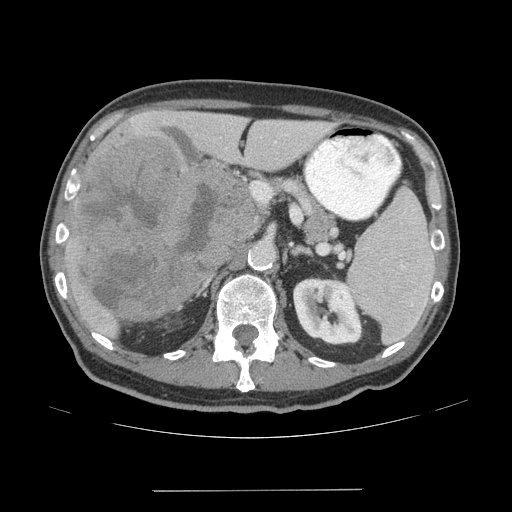
Contrast-enhanced abdominal CT (liver protocol), one axial slice; position 29 of 77 along the scan axis; reconstruction kernel STANDARD; 140 kVp; soft-tissue window (W 400 / L 40 HU); 512 × 512 image matrix, field of view 400 × 400 mm. Case-level facts recorded for this patient, not image findings: diagnosis: hepatocellular carcinoma (patient treated with transarterial chemoembolisation; whether this scan precedes or follows treatment is not stated here); TNM stage (as recorded): Stage-IVA; Child-Pugh class: A; tumour differentiation: well differentiated; tumour nodularity: uninodular.
Outlined on this slice (semi-automatically segmented with operator editing):
- liver parenchyma outside the tumour (the mass and vessels are separate outlines, so this box may not span the whole liver): bounding box <64,110,330,336> (left, top, right, bottom; pixels)
- mass: <72,138,255,320>